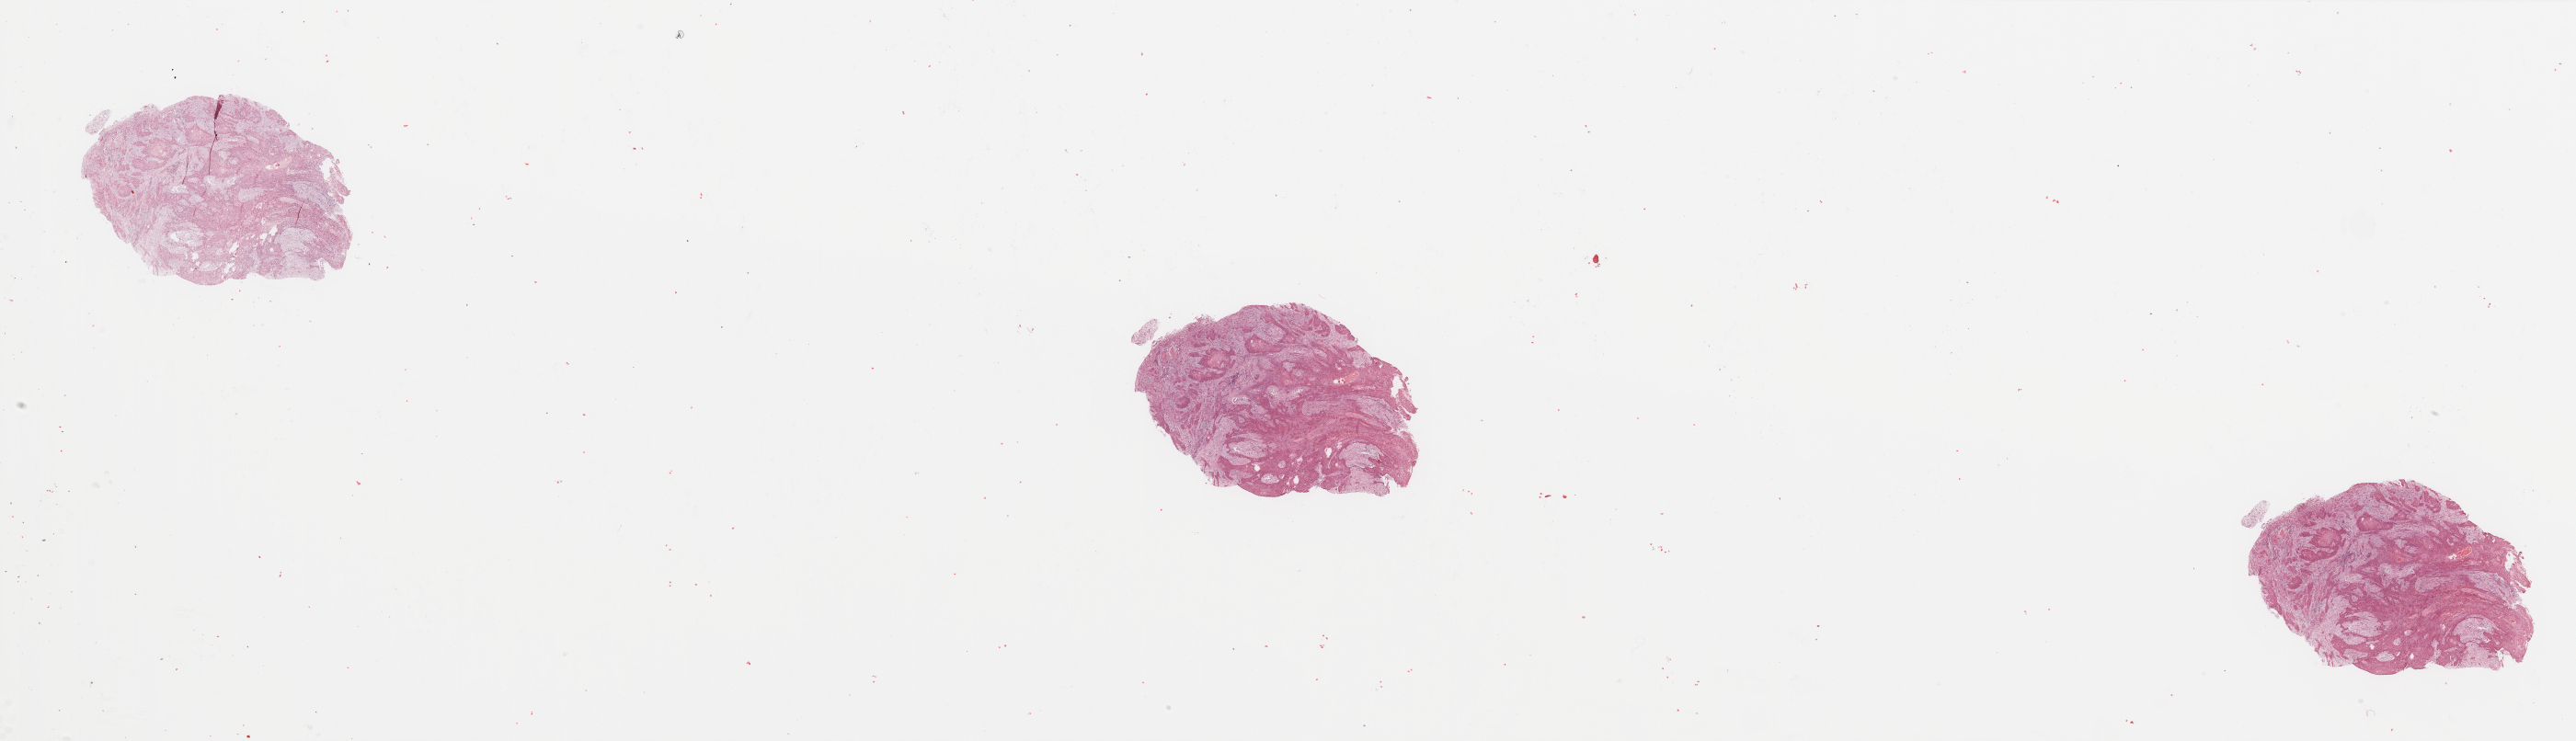
Digitized H&E tissue section (whole slide) — whole scanned area (about 44.3 x 12.7 mm) shown as a low-resolution overview; tumour tissue sample, sampled site: floor of mouth. 65-year-old female patient. Histologic grade: G2 (moderately differentiated). Composition of this section per pathologist review: tumour nuclei 85%, necrosis 3%.
Primary tumour site (as recorded): oral cavity. Diagnosis: Squamous cell carcinoma, NOS (floor of mouth, NOS). AJCC pathologic stage: IVB.